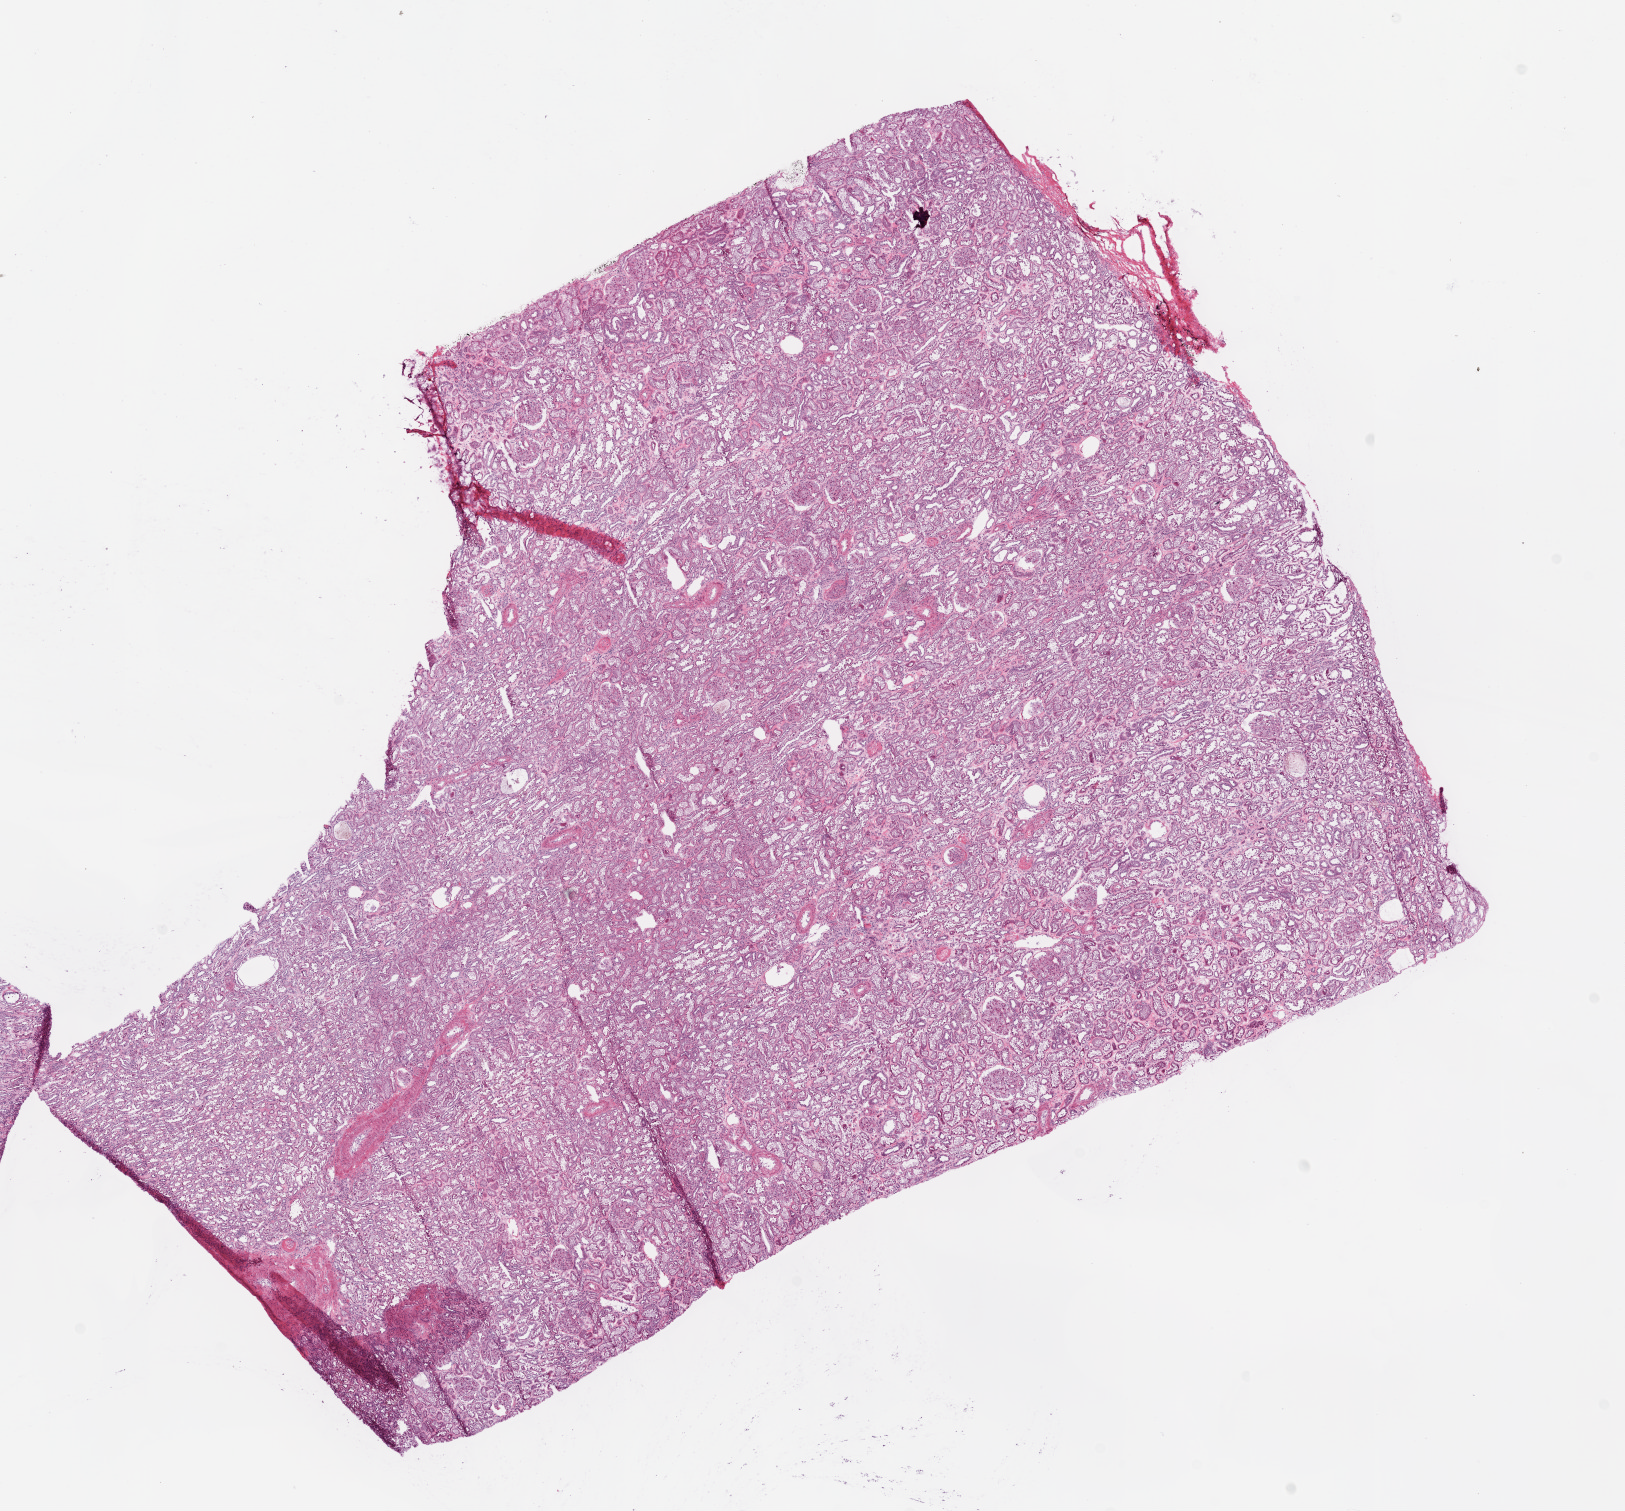
Whole-slide histology image, H&E-stained — shown as a low-resolution overview of the whole scanned area (about 13.0 x 12.1 mm, from a 20x scan). Frozen section from the bottom of the tissue portion. Solid tissue normal (non-tumour tissue) sample from the kidney. Male, age 70 years at initial diagnosis.
This section: solid tissue normal (non-tumour) sample from the same patient. Patient diagnosis: Clear cell adenocarcinoma, NOS.